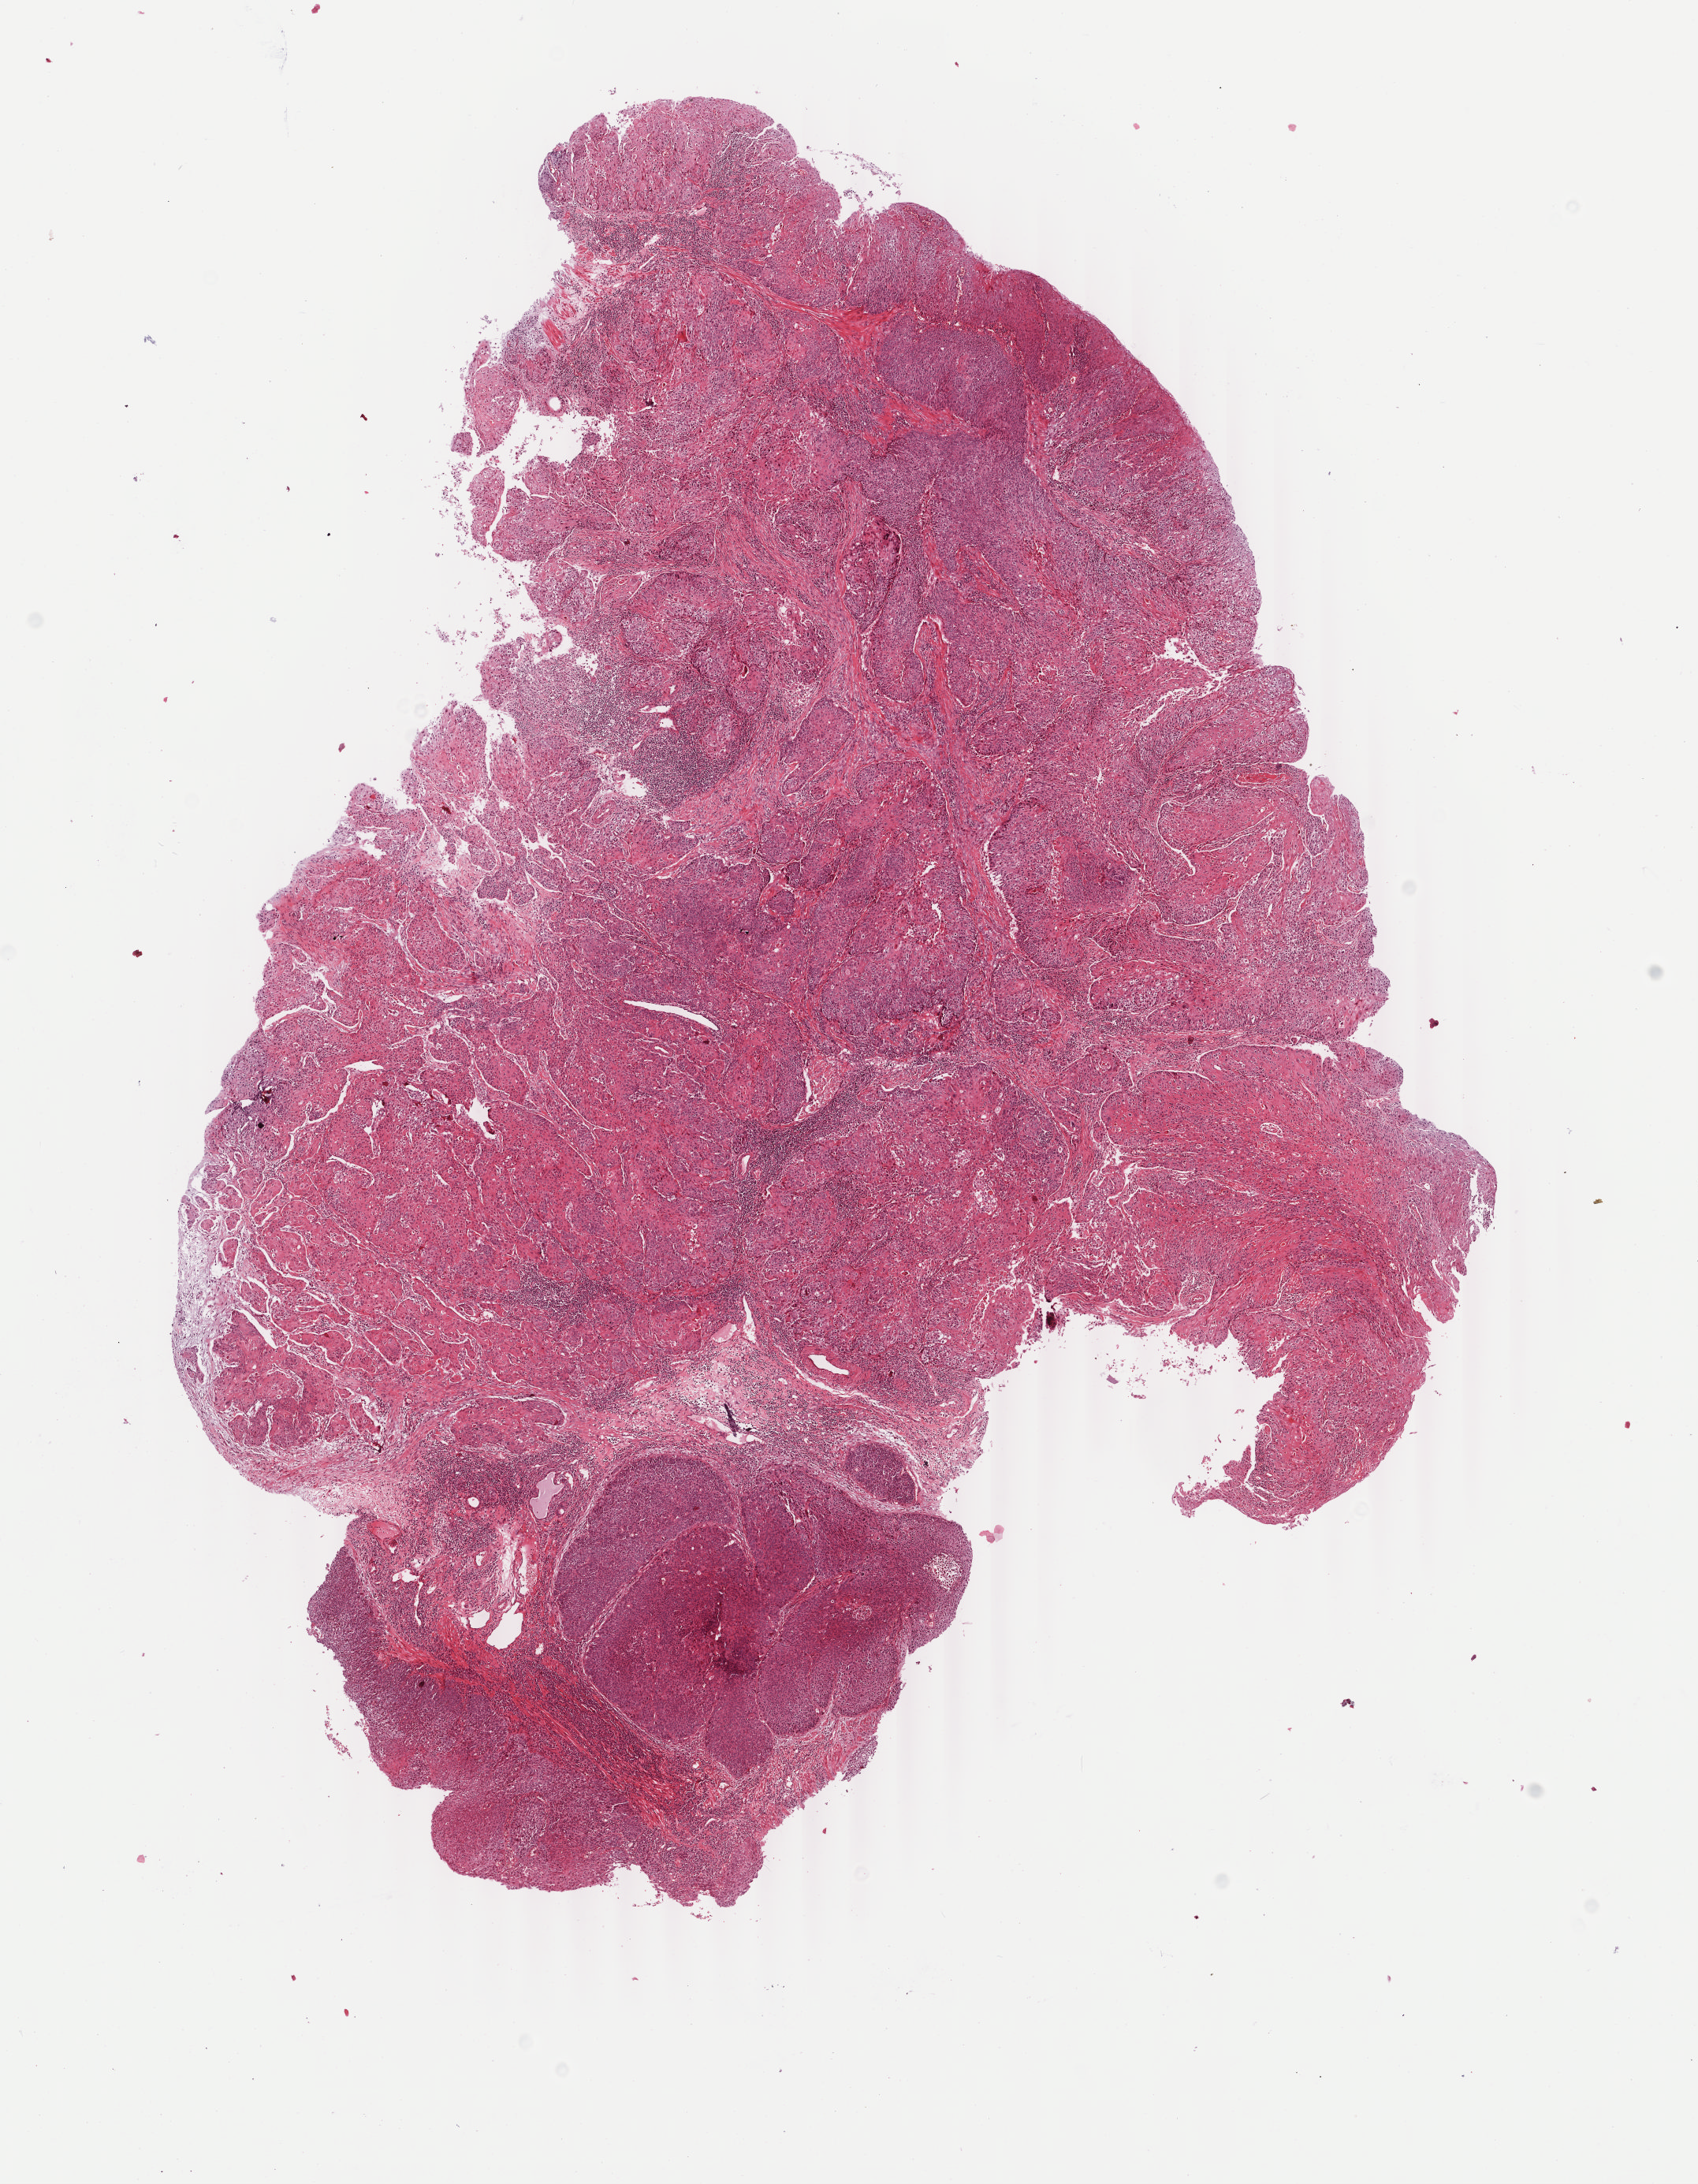
Digitized Hematoxylin and eosin (H&E) stained tissue section (whole slide) — shown as a low-resolution overview of the whole scanned area (about 8.6 x 11.0 mm, slide scanned at 40x). Formalin-fixed paraffin-embedded (FFPE) diagnostic section. Sample: primary tumour, esophagus. Male, age 59 years at initial diagnosis. Histologic grade: G2 (moderately differentiated).
AJCC pathologic stage: IIA (6th edition). Pathologic diagnosis: Squamous cell carcinoma, NOS (lower third of esophagus).